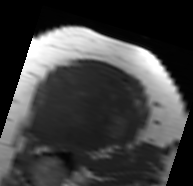
MRI of an extremity soft-tissue mass, one axial slice; position 53 of 91 along the scan axis; MR volume resampled by the dataset authors to the PET/CT grid (not the native acquisition matrix); 3.27 mm slice thickness; 193 × 186 image matrix. Female patient. Case-level facts recorded for this patient, not image findings: histological type: malignant solitary fibrous tumor; grade: intermediate; site of the primary tumour: right thigh.
Structures marked on this image (expert contour drawn on MRI and transferred to this co-registered scan by the dataset authors):
- gross tumour volume including surrounding oedema: bounding box [x1, y1, x2, y2] px = [22, 65, 144, 150]
- gross tumour volume (mass): [24, 67, 139, 150]